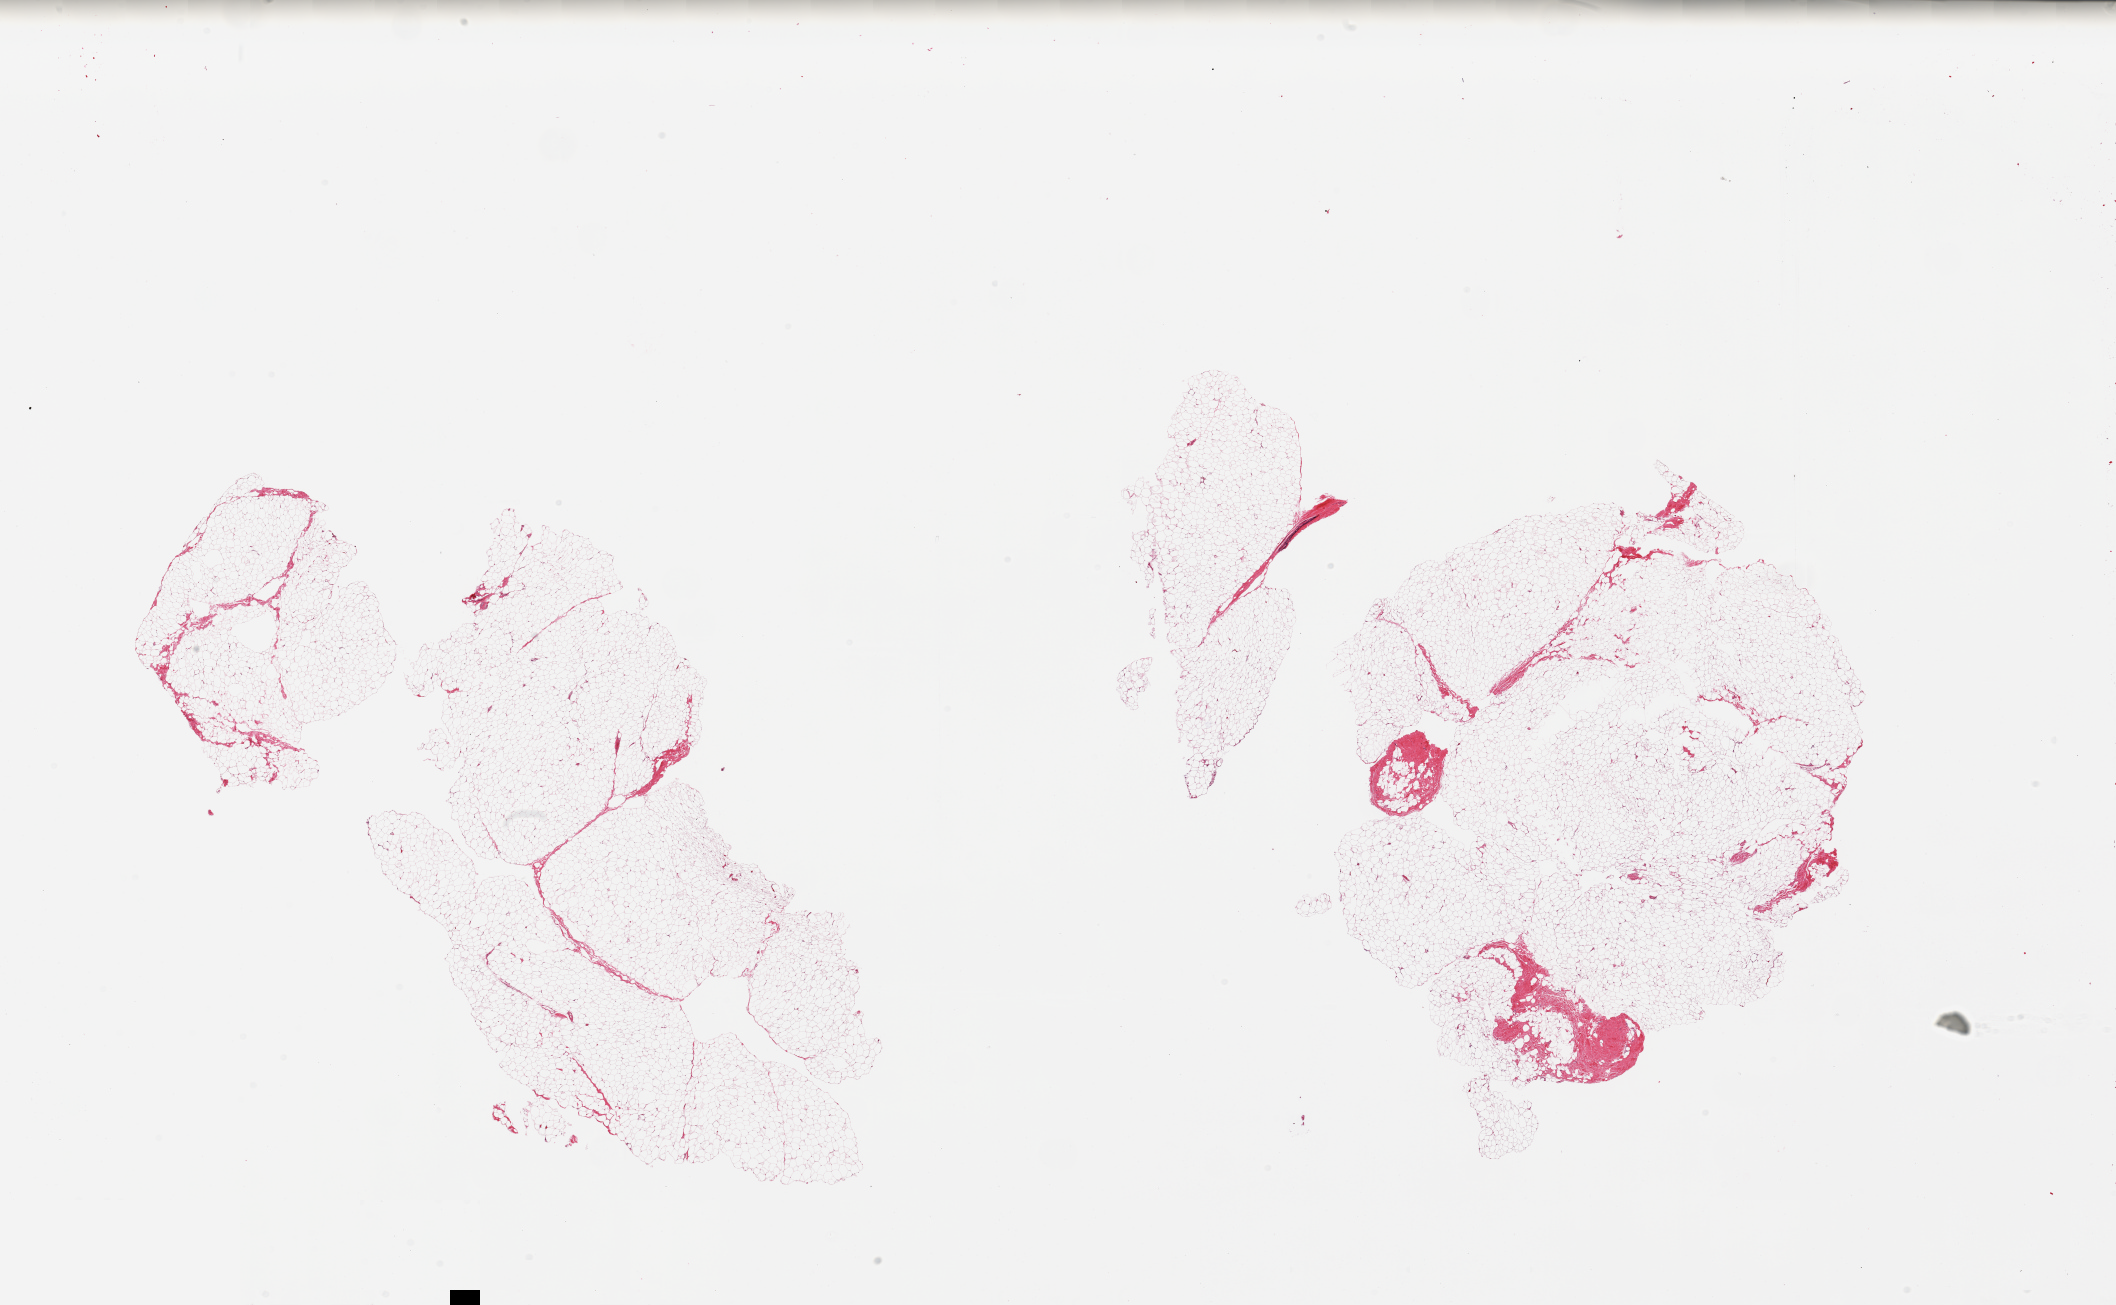
Whole-slide image, H&E stain, brightfield — whole scanned area (about 33.5 x 20.6 mm, slide scanned at 20x) shown as a low-resolution overview. PAXgene-fixed, paraffin-embedded tissue. Sampled site (target tissue): breast. Tissue donor sample. Male donor.
Review note (as recorded): 2 pieces; adipose tissue without mammary ducts.